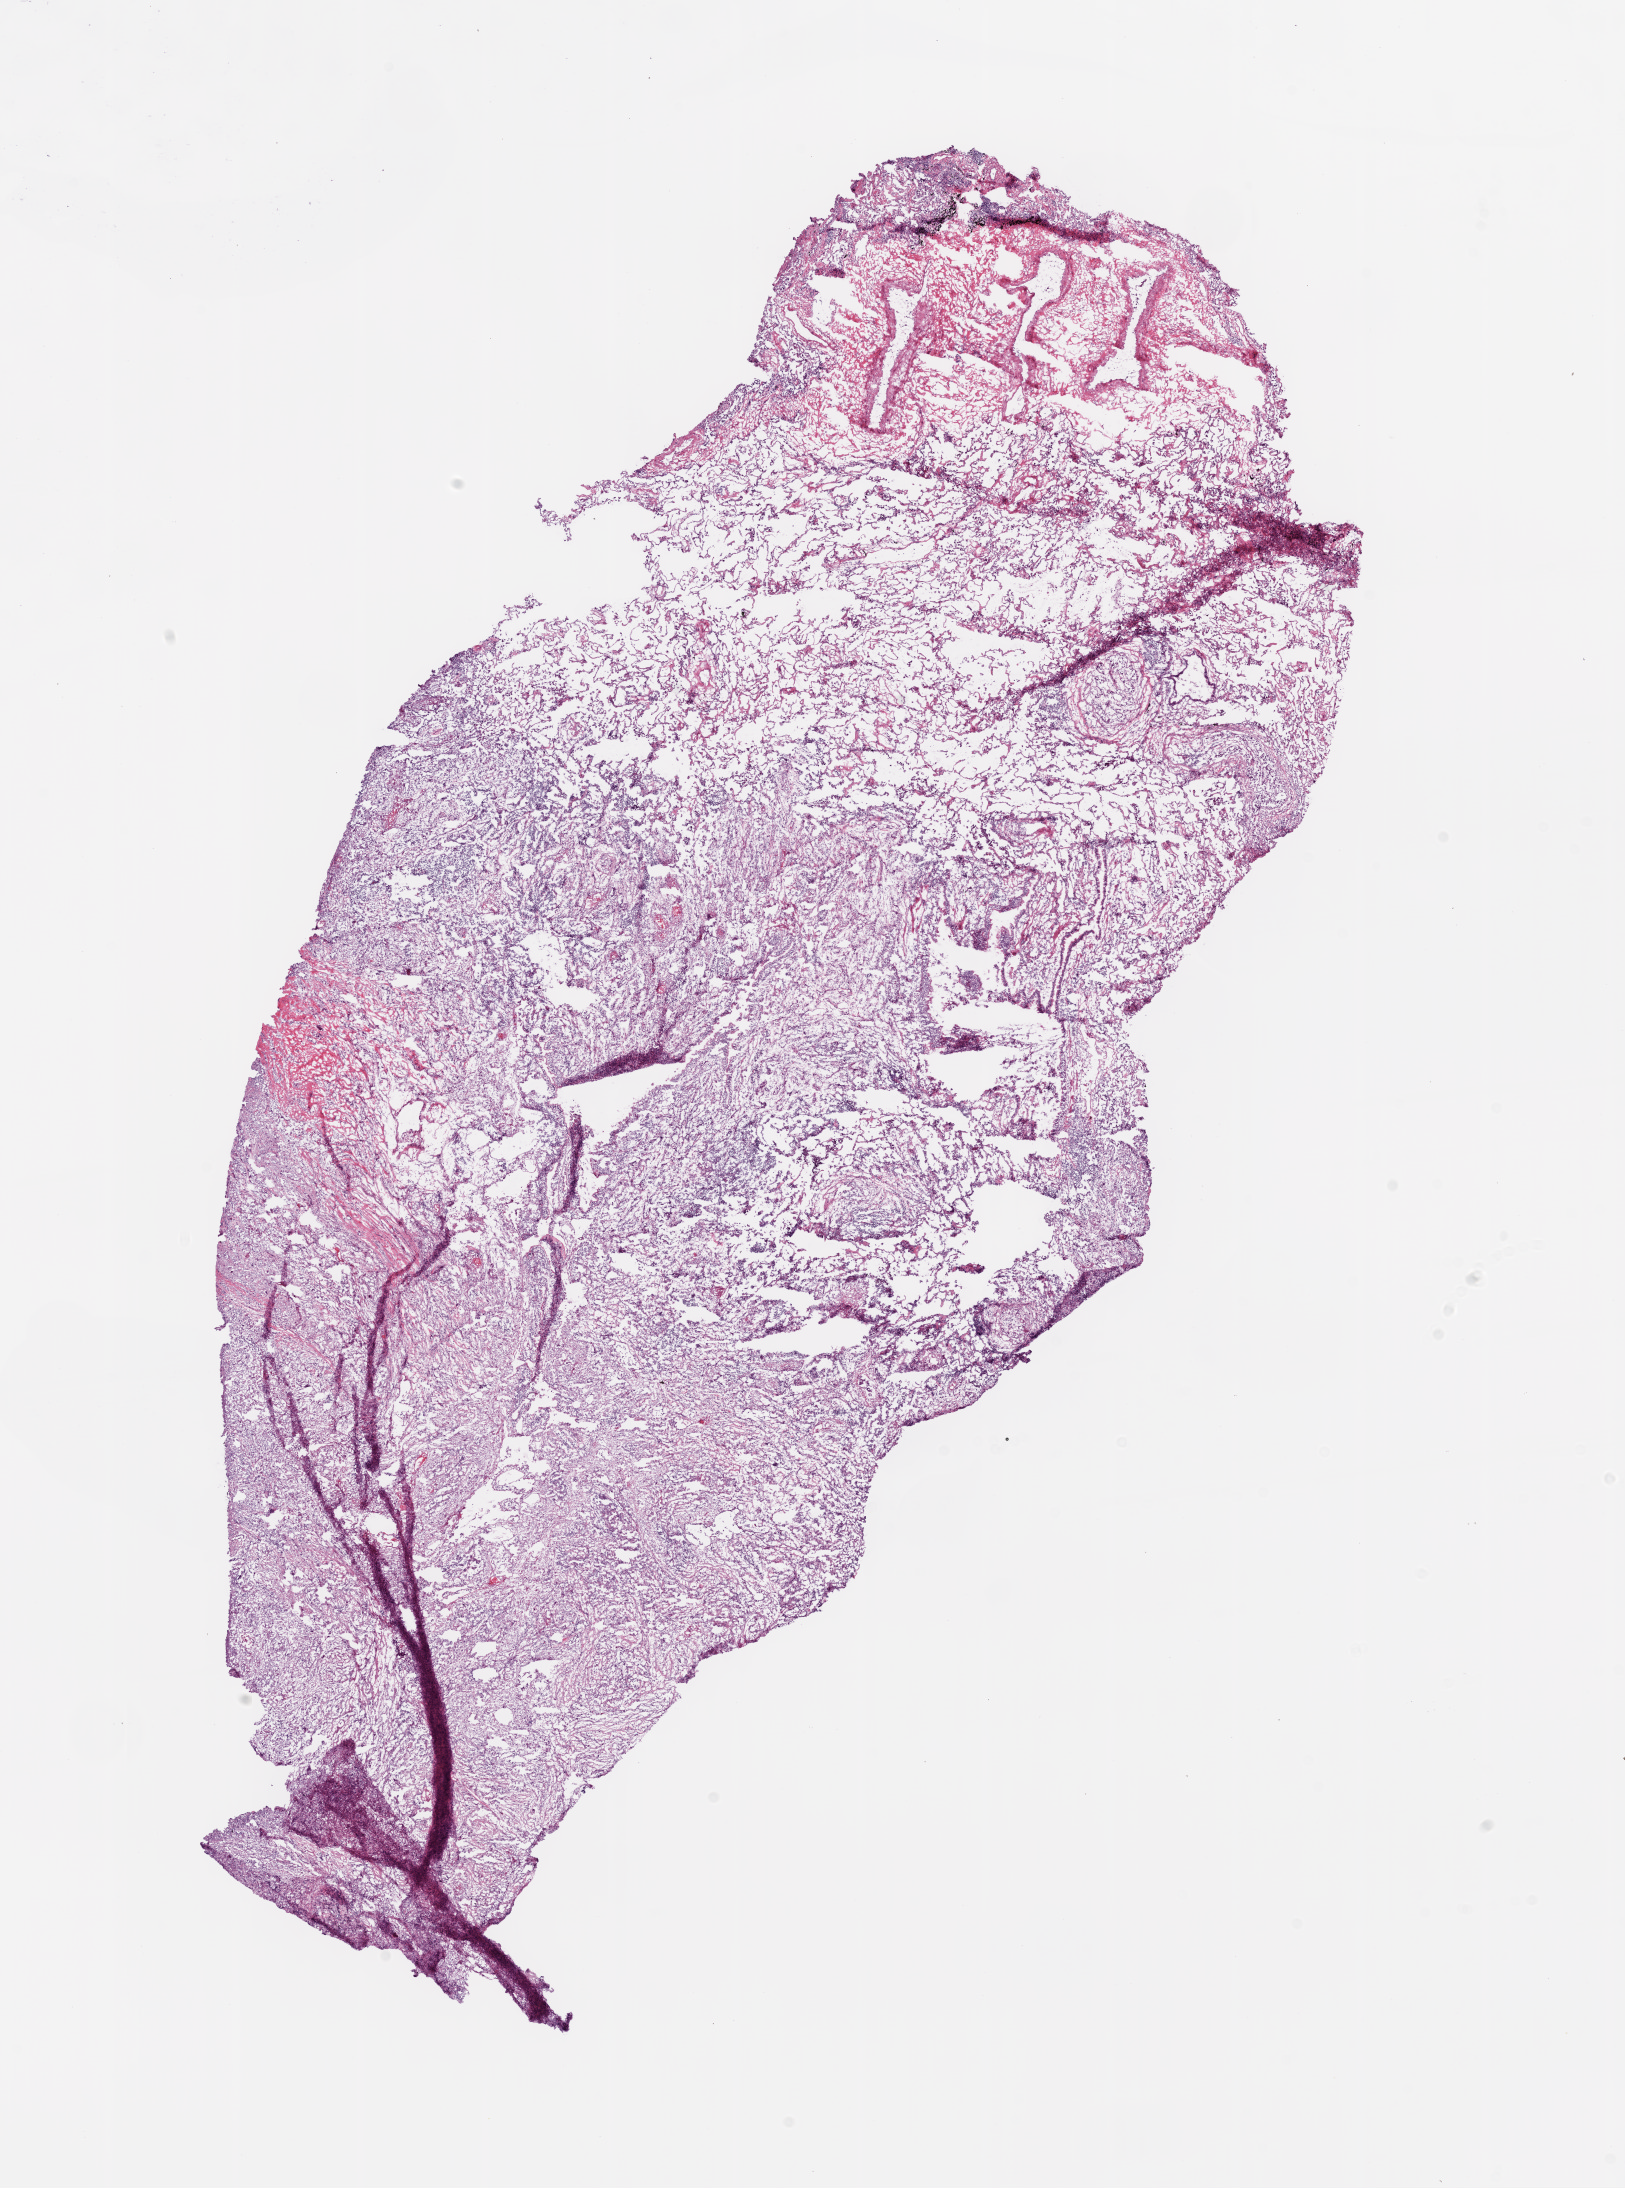
H&E-stained whole-slide image — whole scanned area (about 13.0 x 17.6 mm, from a 20x scan) shown as a low-resolution overview, frozen section, primary tumour sample from the lung. Patient: male, age at initial diagnosis 84 years. Composition of this section per pathologist review: tumour cells 75%, tumour nuclei 75%, normal cells 10%, stromal cells 10%, necrosis 5%. Infiltration values recorded for this section: lymphocyte infiltration 10%, monocyte infiltration 5%.
AJCC pathologic stage: IB. Diagnosis: Squamous cell carcinoma, NOS (upper lobe, lung).